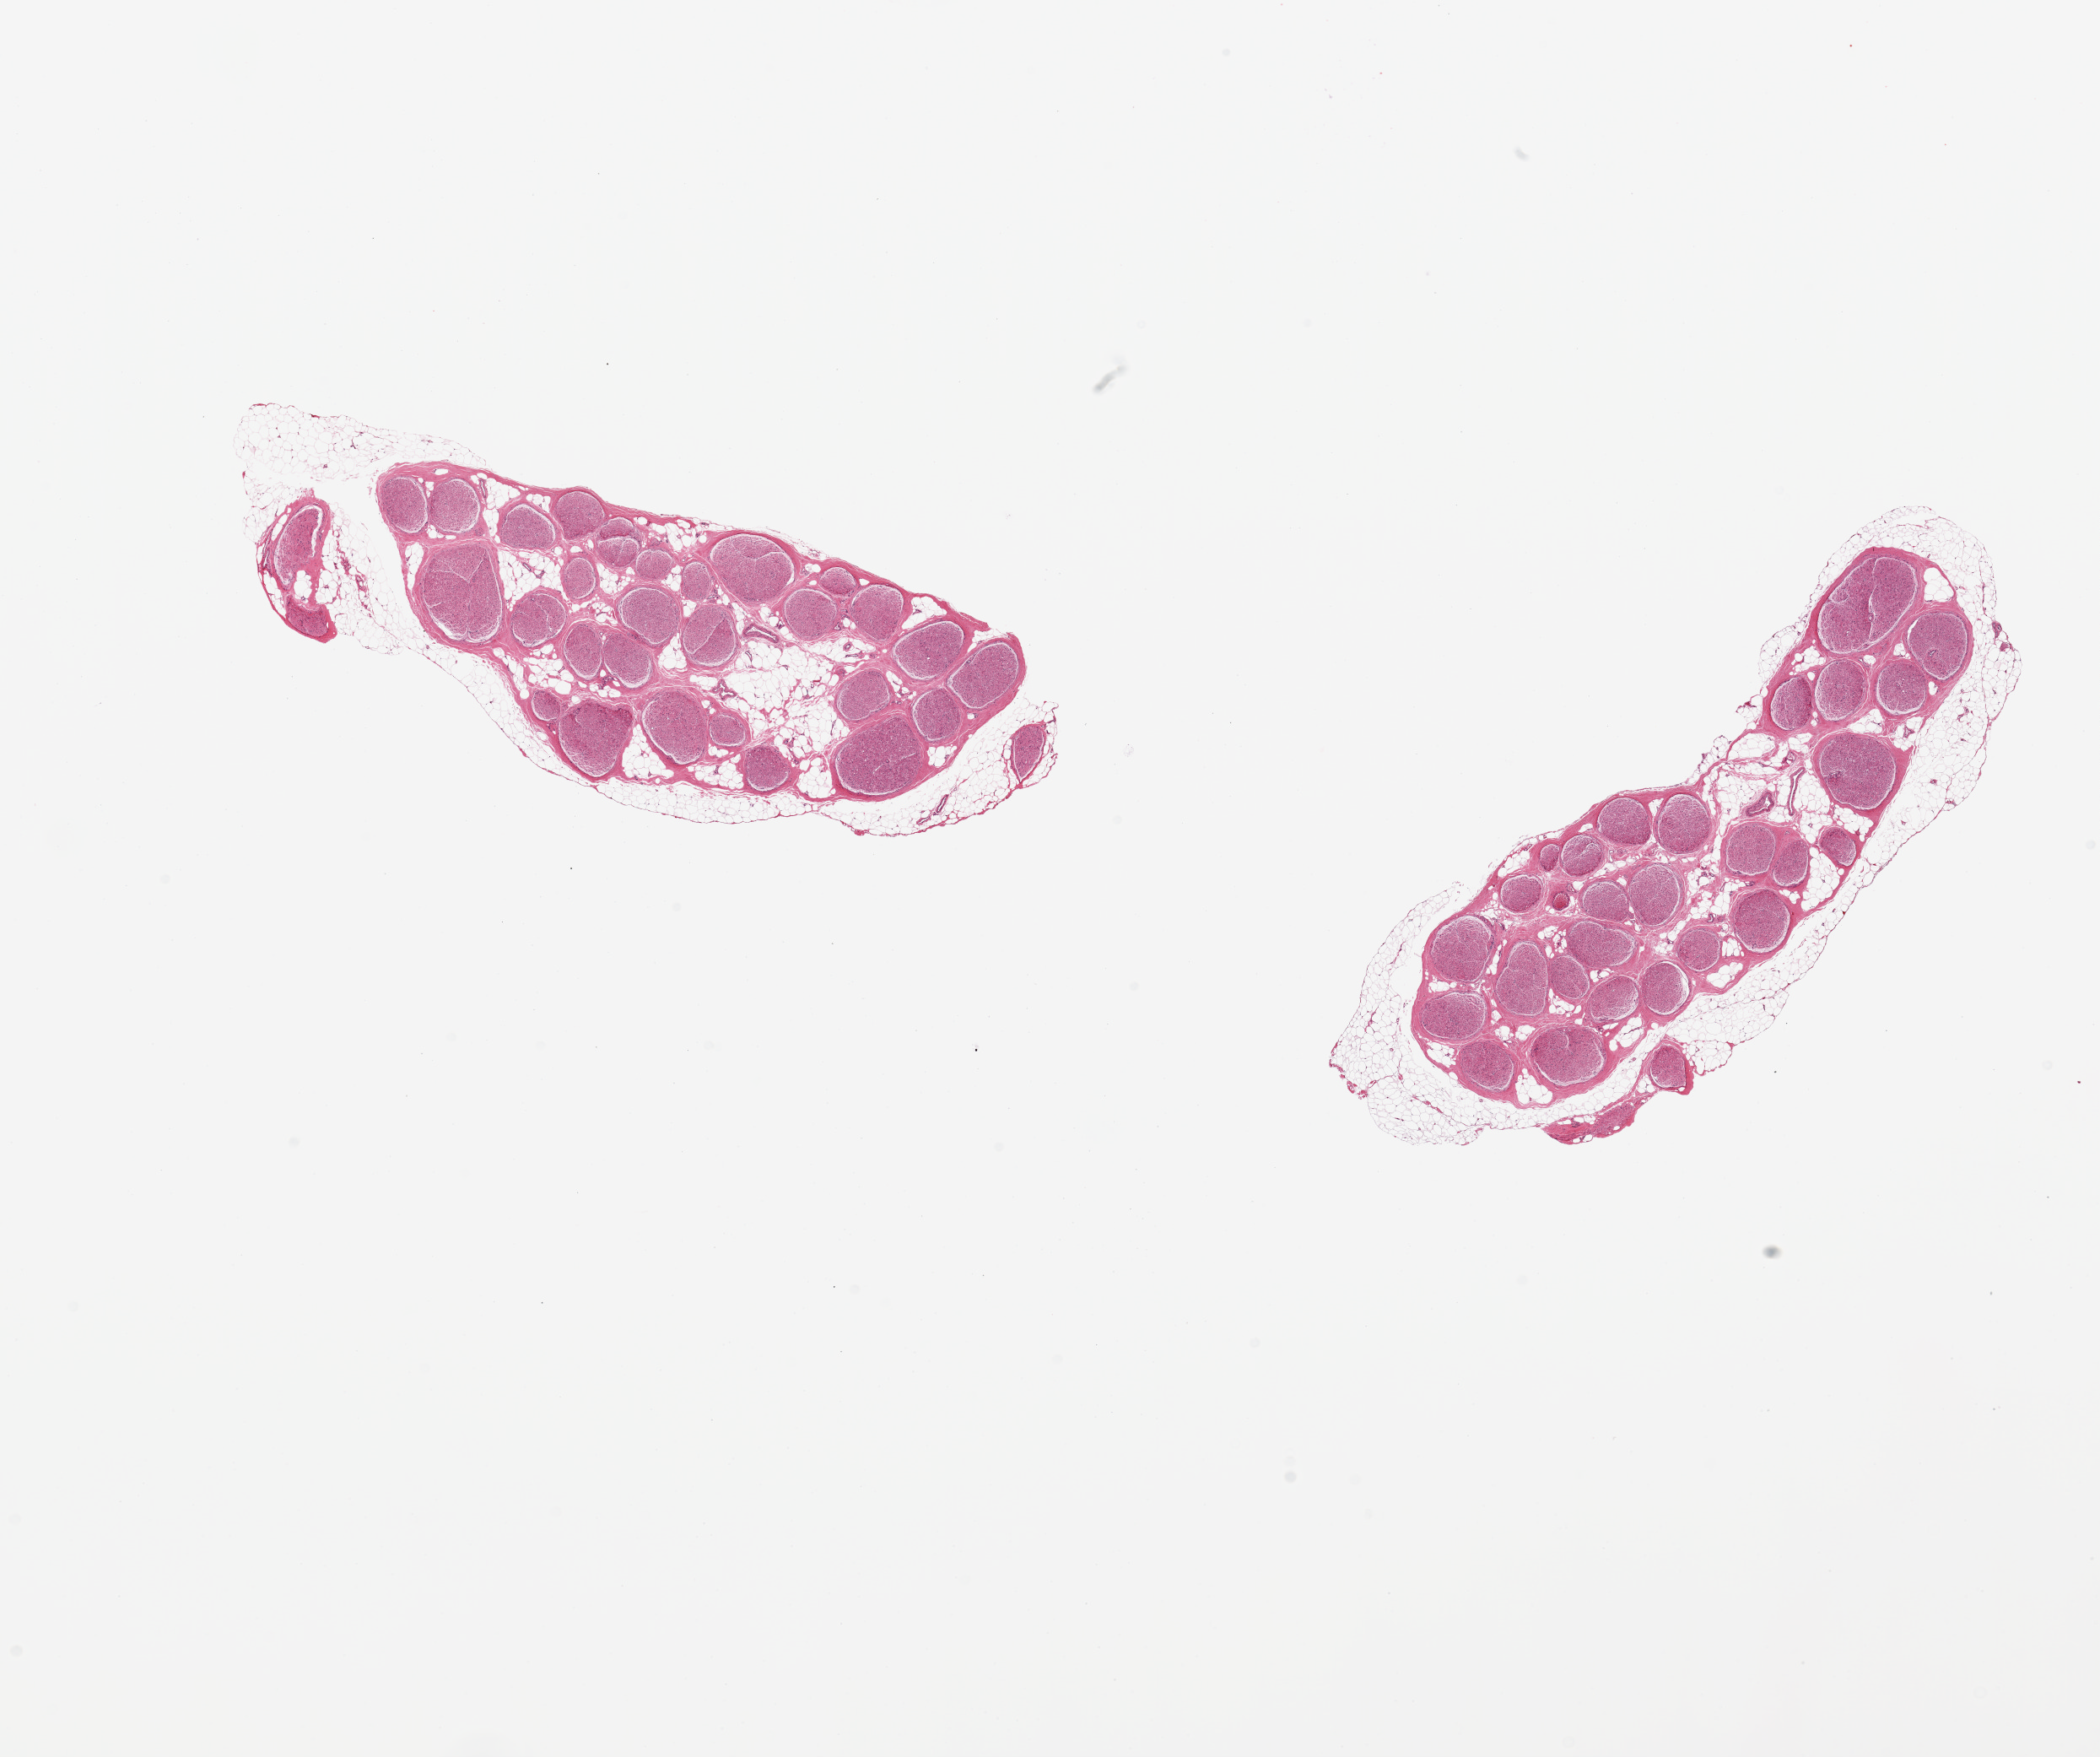
Whole-slide image, hematoxylin and eosin (H&E) stain, a low-resolution overview of the entire scanned area, about 19.7 x 16.5 mm (slide scanned at 20x); PAXgene-fixed paraffin-embedded (PFPE) section; section of tibial nerve (target tissue); donor tissue sample. Female donor.
Pathologist's review note for this sample: 2 pieces; both include ~25% internal and external fat combined.